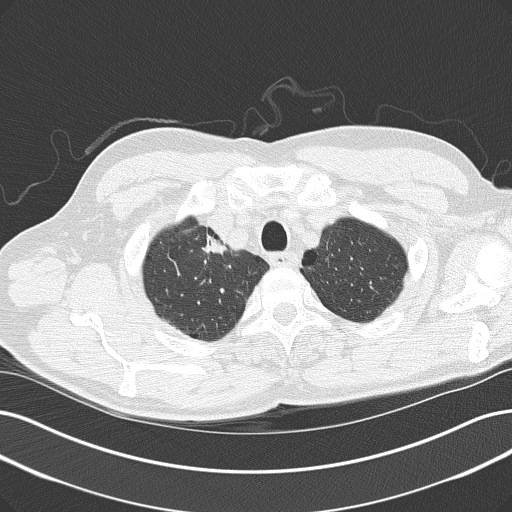
Low-dose screening chest CT, axial slice, baseline screening round, lung window (W 1500 / L -600 HU), 2 mm slice thickness, lung (sharp) reconstruction kernel (B50f), 512 × 512 image matrix, field of view 365 × 365 mm. Male, age 61 years at enrolment. Current smoker at enrolment.
Expert-annotated lung lesion, bounding box <192,227,245,272> (left, top, right, bottom; pixels). The screening reader recorded 2 non-calcified nodules or masses ≥4 mm on this exam (right upper lobe, right upper lobe); which of them this box marks is not recorded. Official screen result: positive, change unspecified: nodule(s) >= 4 mm or enlarging nodule(s), mass(es), or other non-specific abnormalities suspicious for lung cancer. Participant outcome: lung cancer diagnosed 54 days after this screen — adenocarcinoma, NOS, right upper lobe, poorly differentiated (G3), stage IIIB (AJCC 6th edition).